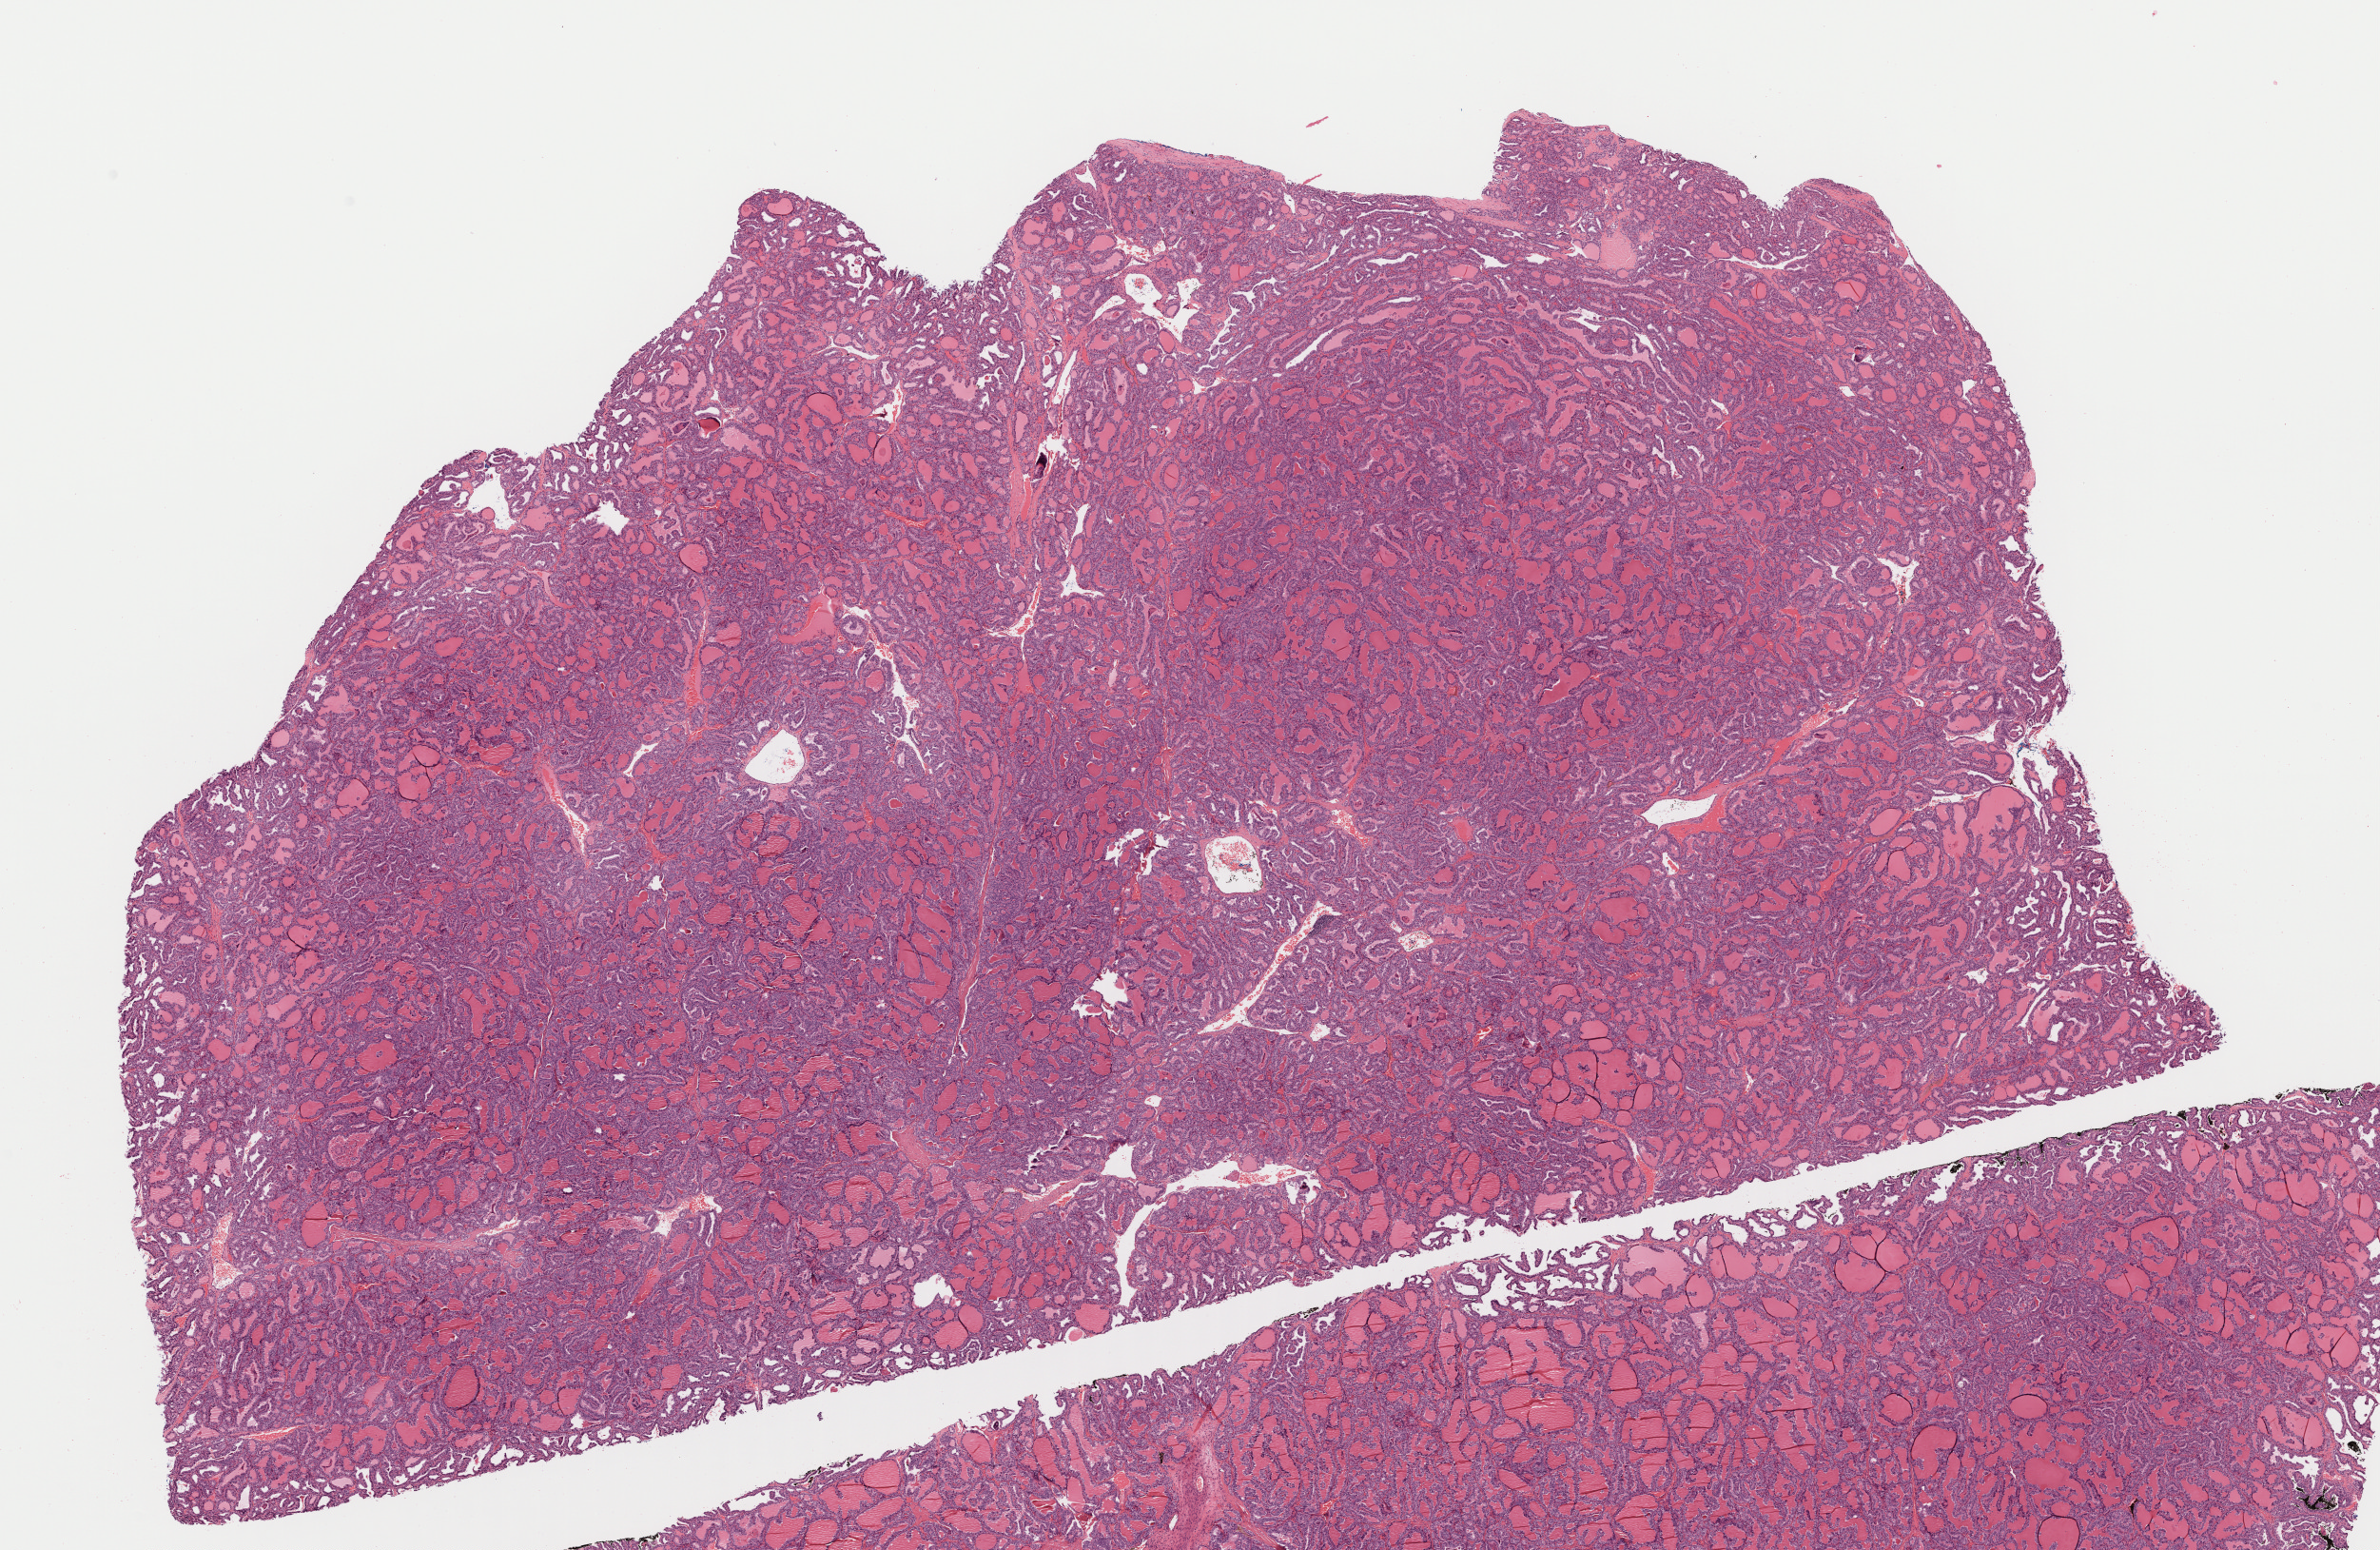
Digitized H&E tissue section (whole slide), shown as a low-resolution overview of the whole scanned area (about 20.2 x 13.1 mm, acquisition: 40x scan), formalin-fixed paraffin-embedded (FFPE) diagnostic section, thyroid, primary tumour sample. Male patient; age at initial diagnosis 28 years.
Lymph nodes positive (case pathology): 3 of 3 examined. Pathologic diagnosis: Papillary adenocarcinoma, NOS (thyroid gland). AJCC pathologic stage: I (7th edition).